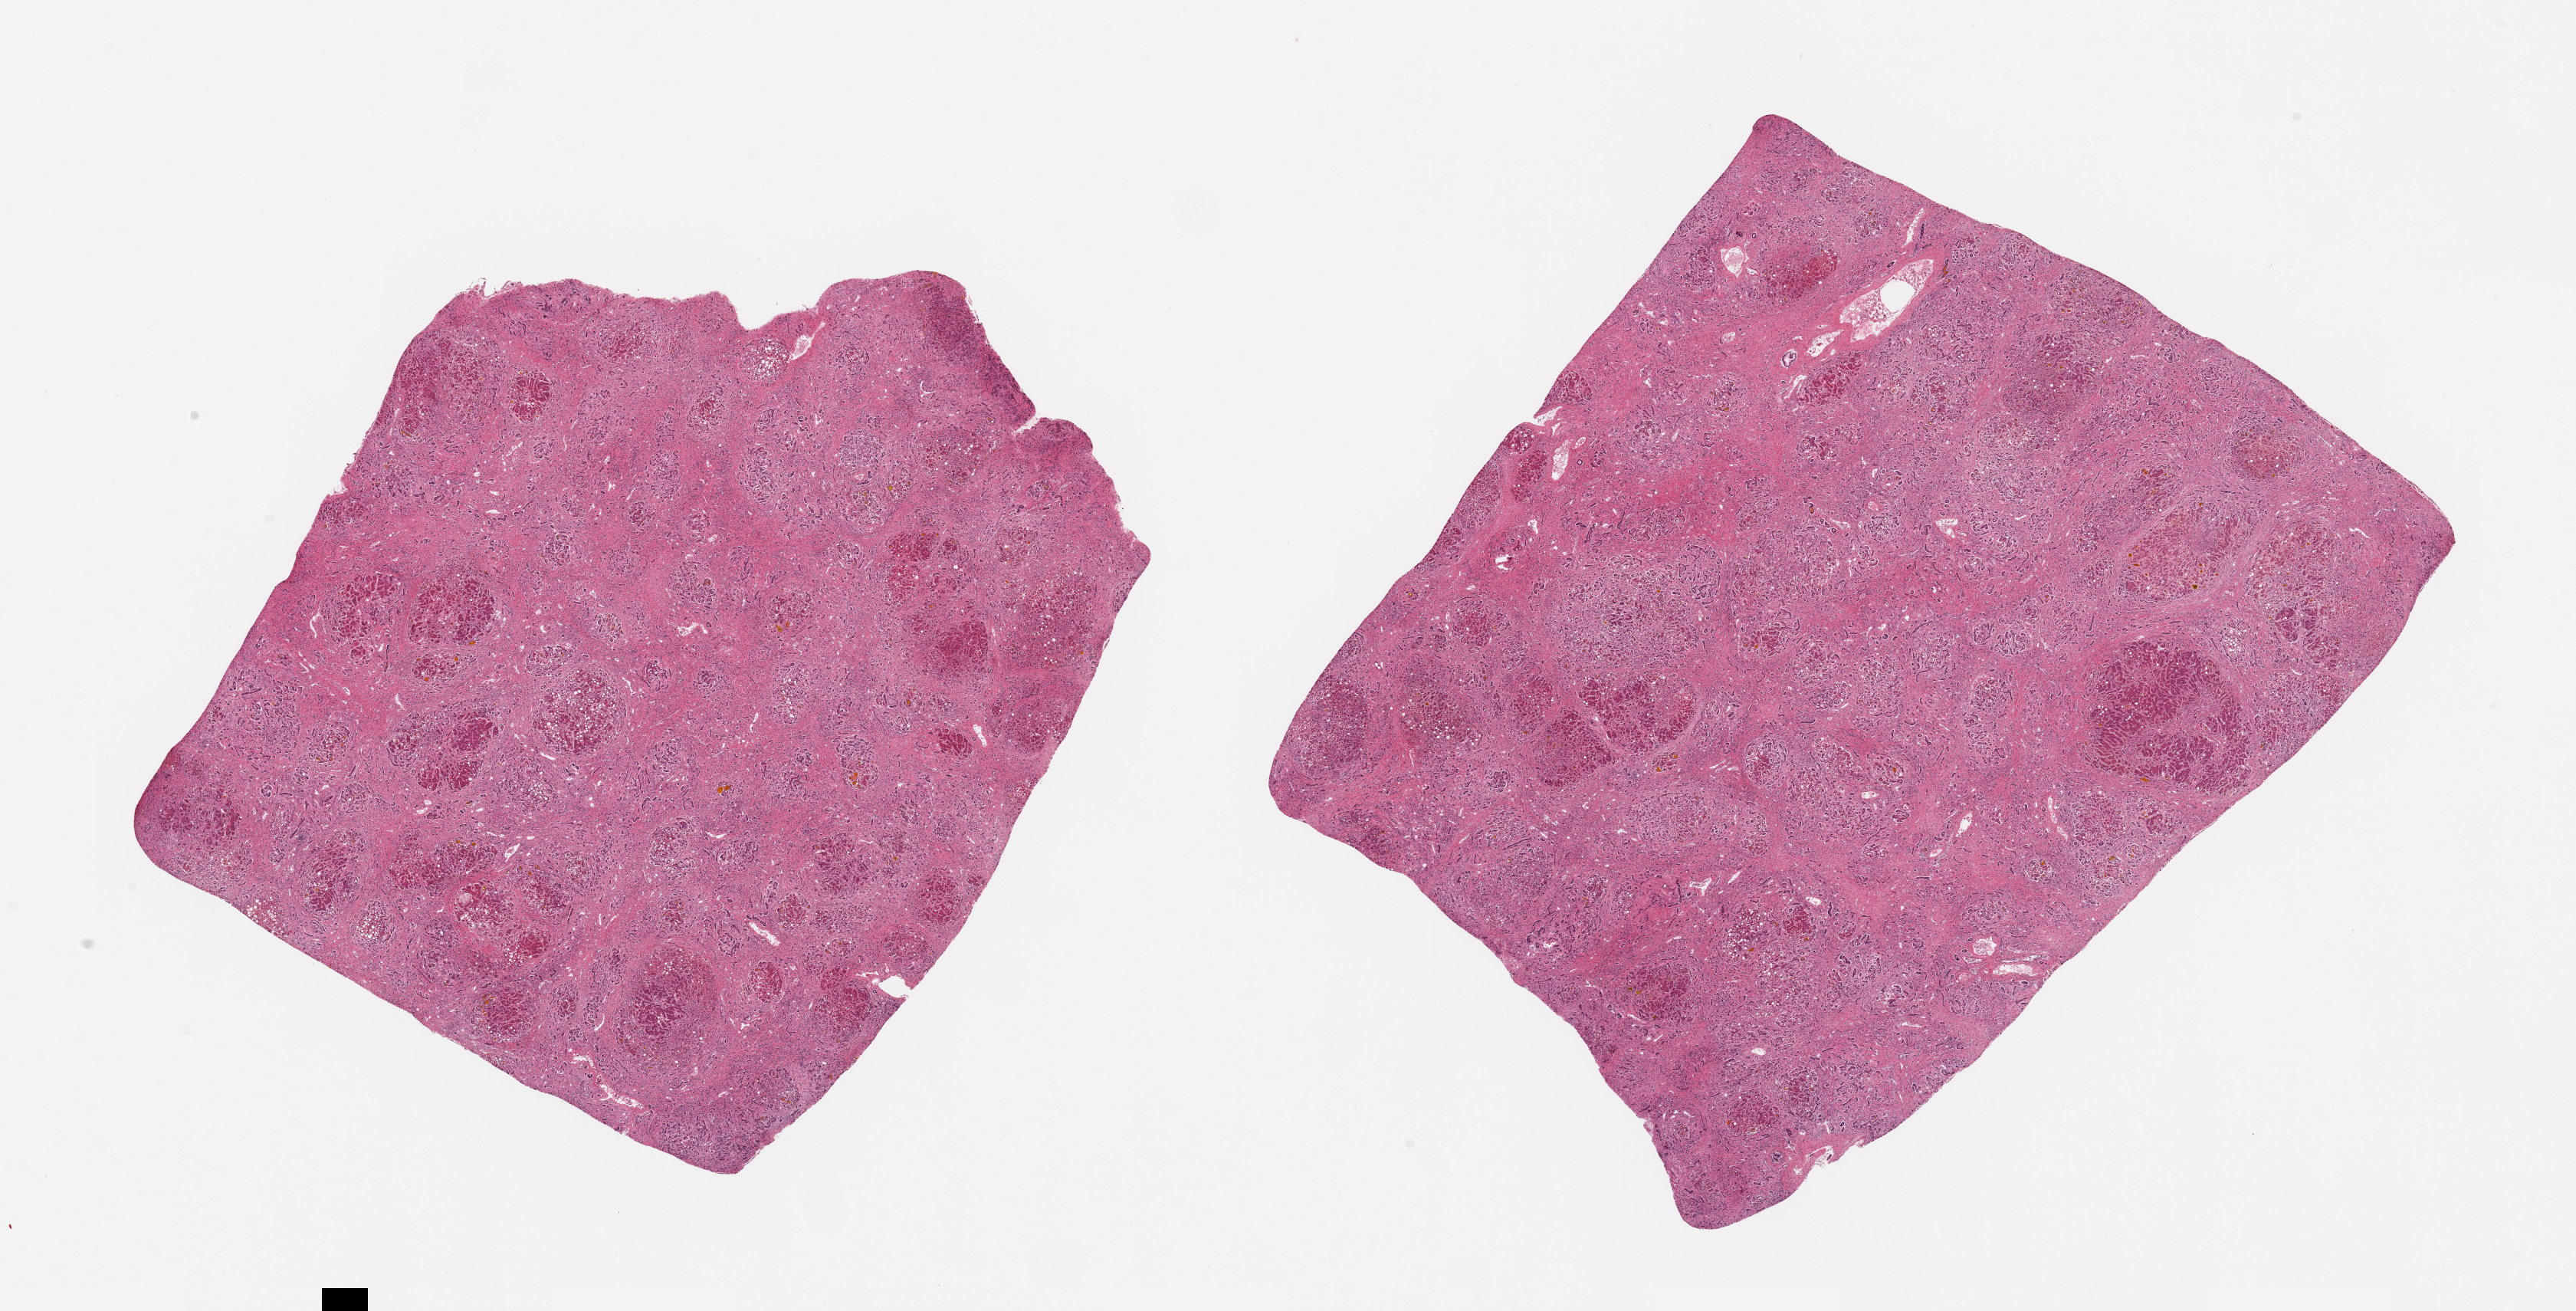
Hematoxylin and eosin (H&E) whole-slide image, brightfield, low-resolution overview of the scanned area, about 26.6 x 13.5 mm. PAXgene-fixed, paraffin-embedded tissue. Section of liver (target tissue). Tissue donor sample. Donor sex: male.
* review note (as recorded): 2 pieces; consistent with advanced alcoholic cirrhosis: steatosis, Mallory's hyaline, extensive fibrosis, marked cholestasis